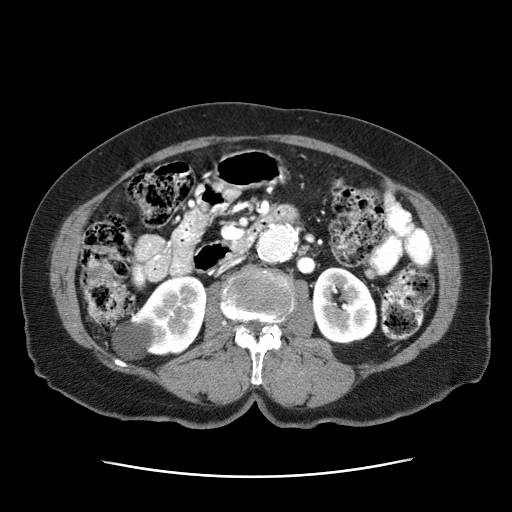
Contrast-enhanced abdominal CT (liver protocol), one axial slice; position 3 of 63 along the scan axis; reconstruction kernel STANDARD; 120 kVp; intravenous contrast given; soft-tissue window (W 400 / L 40 HU); 512 × 512 image matrix. Female patient, age 79 years. From the clinical record (not read from this slice): diagnosis: hepatocellular carcinoma (patient treated with transarterial chemoembolisation; whether this scan precedes or follows treatment is not stated here); TNM stage (as recorded): Stage-II.
Annotated regions visible in this slice (semi-automatically segmented with operator editing):
- abdominal aorta: bounding box [x1, y1, x2, y2] px = [257, 226, 297, 263]